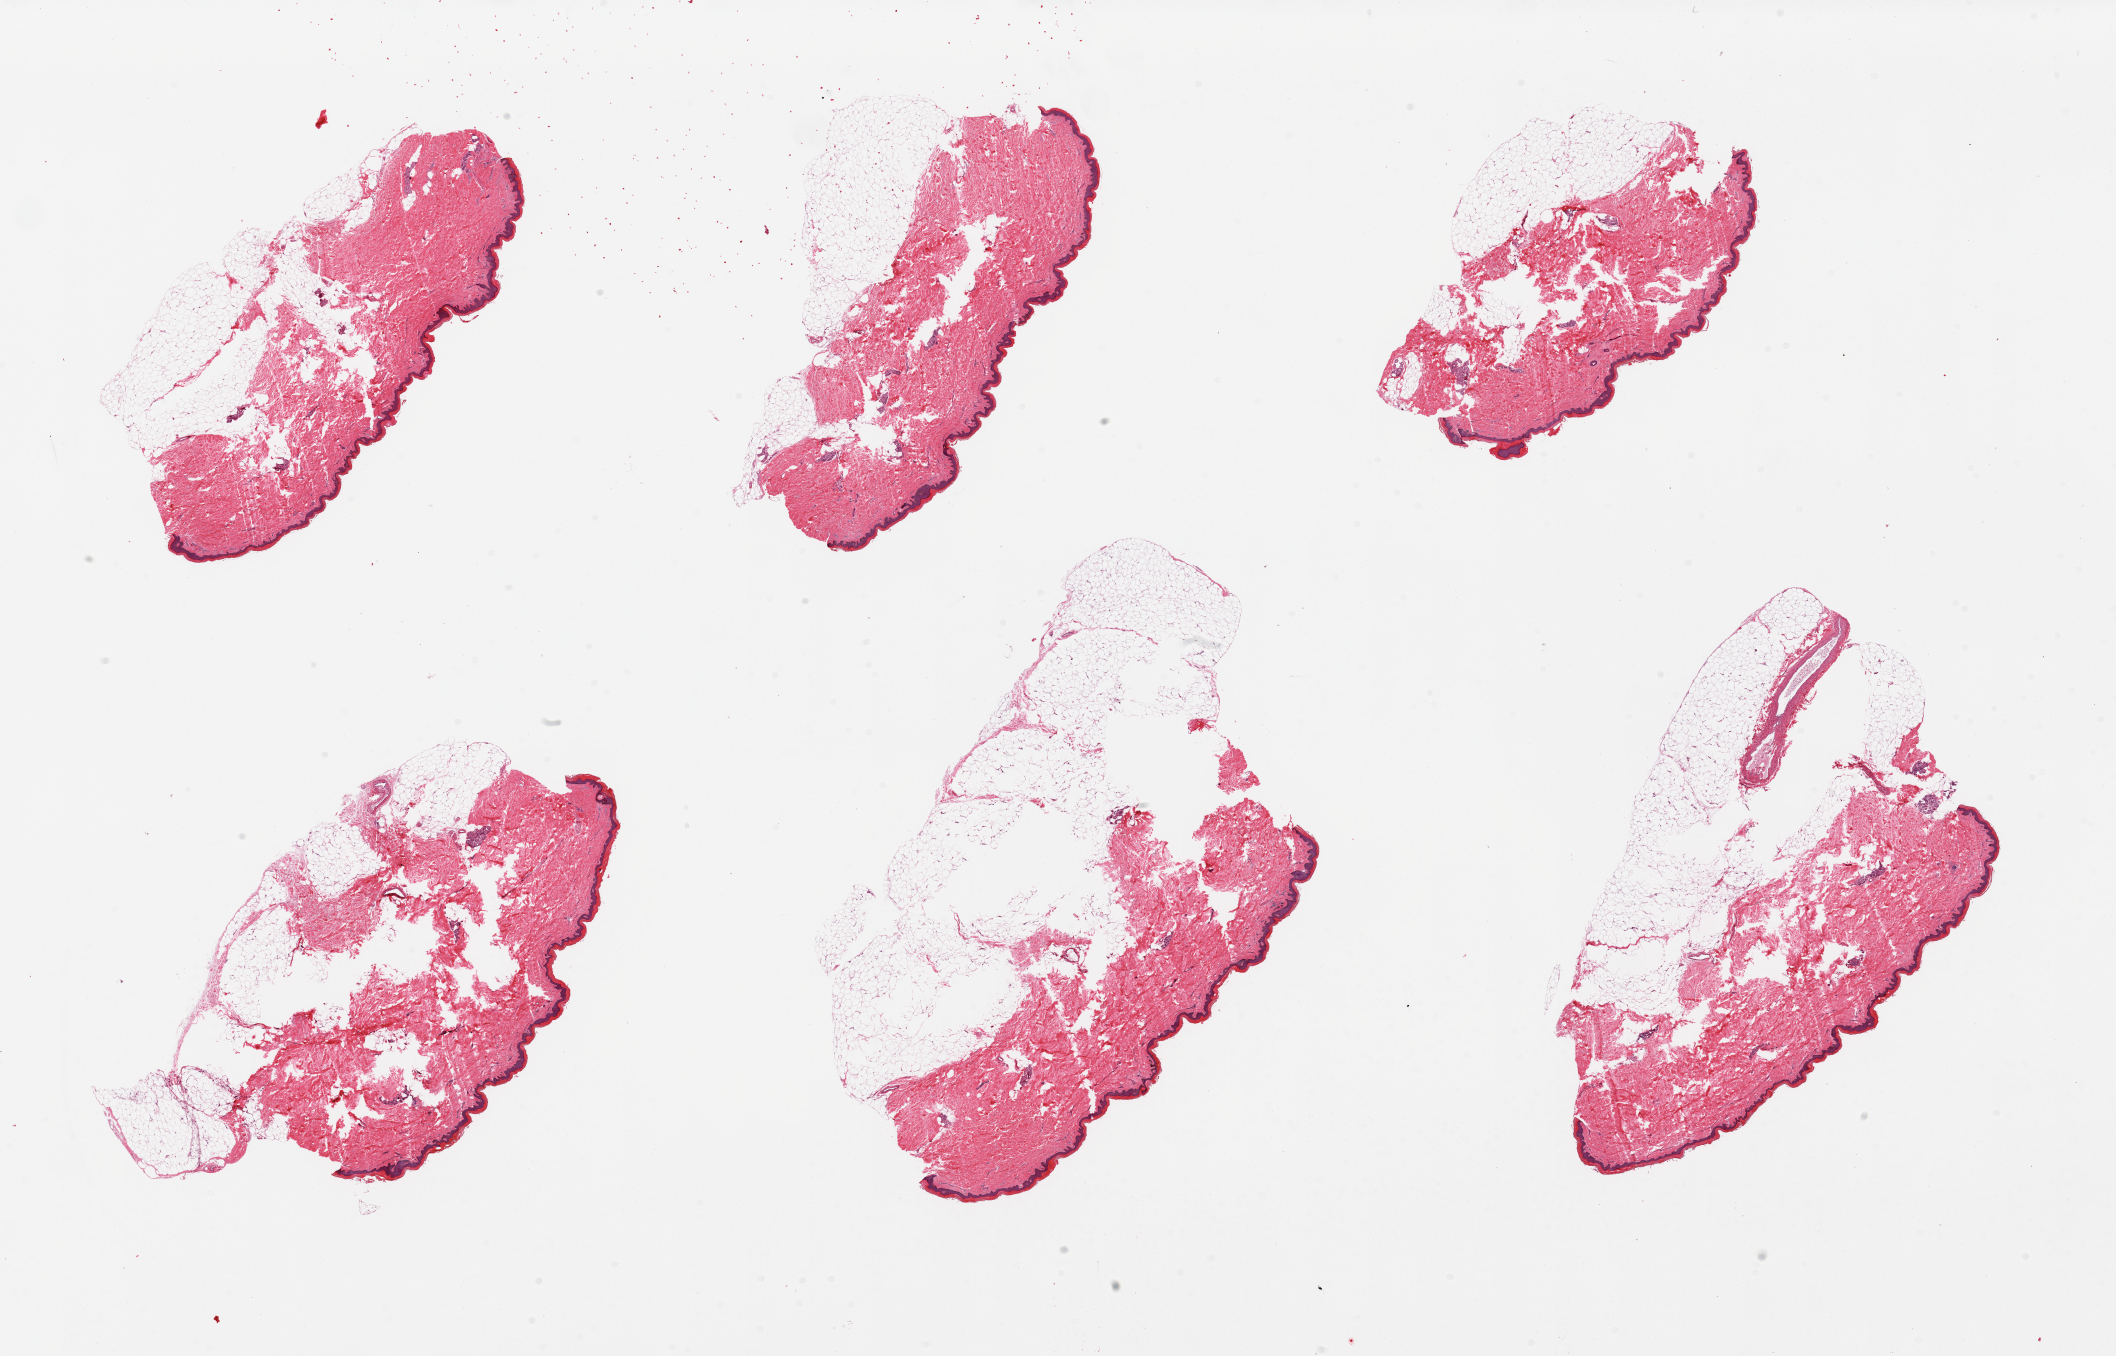
Whole-slide image, haematoxylin and eosin stain, a low-resolution overview of the entire scanned area, about 33.5 x 21.4 mm. PAXgene-fixed, paraffin-embedded tissue. Sampled site (target tissue): skin of lower leg. Donor tissue sample. Donor sex: male.
Reviewer comment on this tissue sample: 6 pieces, each with attached adipose tissue from 20-50%, squamous epithelium measures 30-50 microns thick.